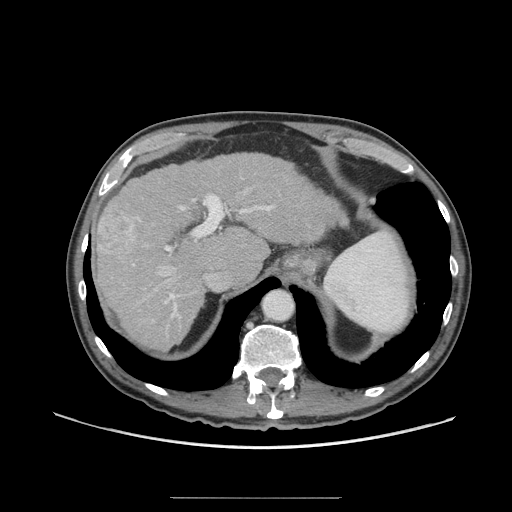
Contrast-enhanced abdominal CT (liver protocol), one axial slice. Position 50 of 71 along the scan axis. Reconstruction kernel STANDARD. Soft-tissue window (W 400 / L 40 HU). 2.5 mm slice thickness. 512 × 512 image matrix, field of view 400 × 400 mm. From the clinical record (not read from this slice): diagnosis: hepatocellular carcinoma (patient treated with transarterial chemoembolisation; whether this scan precedes or follows treatment is not stated here); TNM stage (as recorded): Stage-I; Child-Pugh class: A.
Annotated regions visible in this slice (semi-automatically segmented with operator editing):
- abdominal aorta: bounding box (x1, y1, x2, y2) in pixels: (264, 291, 293, 320)
- liver parenchyma outside the tumour (the mass and vessels are separate outlines, so this box may not span the whole liver): (96, 152, 340, 348)
- mass: (95, 204, 141, 262)
- liver vessels: (132, 195, 274, 317)